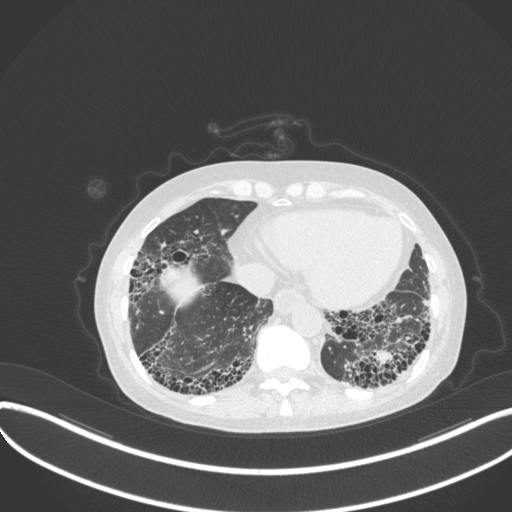
Chest CT, one axial slice. Position 76 of 373 along the scan axis. Lung window (W 1500 / L -600 HU). 1 mm slice thickness. 512 × 512 image matrix. Patient: female, 56 years. From the clinical record (not read from this slice): clinical TNM (as recorded): T1 N0 M0.
Structures marked on this image (rectangle marked by the reading radiologist):
- lung tumour (recorded histology: adenocarcinoma): bounding box [x1, y1, x2, y2] px = [370, 346, 396, 373]